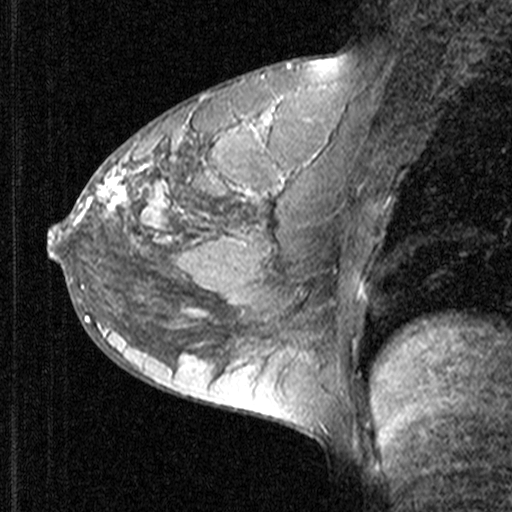
Breast MRI (dynamic contrast-enhanced), one sagittal slice. Dynamic contrast-enhanced study with each time point stored as its own series, time point 2 of 3 at this slice position (early post-contrast, ordered by acquisition time). 1.5 T. TE 4.5 ms, TR 11 ms. 3 mm slice thickness. 512 × 512 image matrix, field of view 200 × 200 mm. Patient: female, 27 years. From the clinical record (not read from this slice): setting: breast cancer imaged before/during neoadjuvant chemotherapy; receptor status: HR-positive, HER2-negative.
Structures marked on this image (semi-automatically segmented with operator editing):
- analysis volume of interest (the breast-tissue region the enhancement analysis was run in; not a lesion): box from (x=68, y=146) to (x=165, y=239) px
- tumour enhancement mask (voxels above the 90 % enhancement threshold inside the analysis volume of interest): (x=71, y=179)–(x=158, y=235)